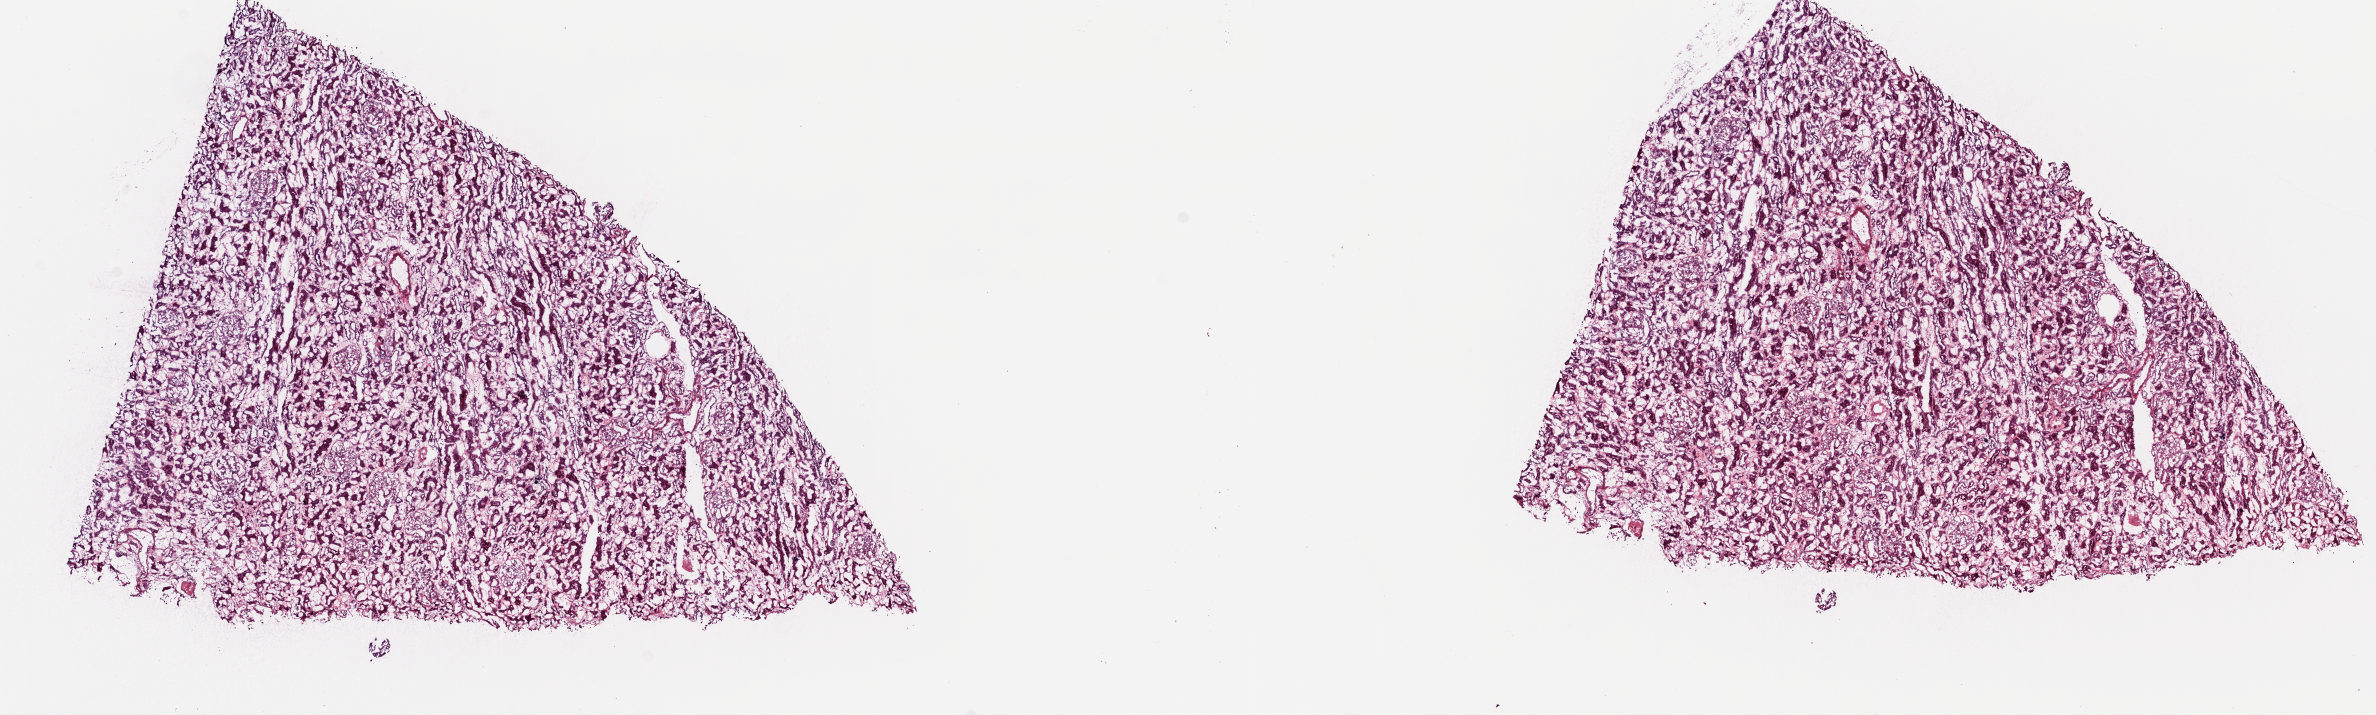
H&E-stained whole-slide image, low-resolution overview of the scanned area, about 18.8 x 5.7 mm; frozen section from the top of the tissue portion; sample: solid tissue normal (non-tumour tissue), kidney. Male, age 40 years at initial diagnosis. Pathologist review of this section (percent, as recorded): tumour cells 0%, tumour nuclei 0%, normal cells 70%, stromal cells 30%, necrosis 0%. Inflammatory infiltration, as recorded: lymphocyte infiltration 2%, monocyte infiltration 1%, neutrophil infiltration 1%.
- this section: solid tissue normal (non-tumour) sample from the same patient
- patient diagnosis: Papillary adenocarcinoma, NOS